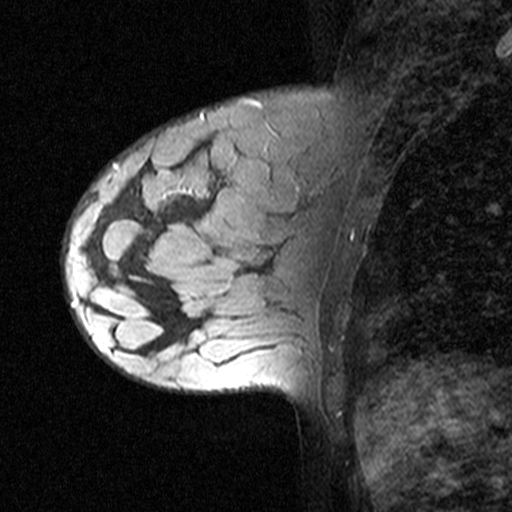
Breast MRI (dynamic contrast-enhanced), one sagittal slice; position 14 of 44 along the scan axis; dynamic contrast-enhanced study with each time point stored as its own series, time point 2 of 3 at this slice position (early post-contrast, ordered by acquisition time); 1.5 T; TE 4.5 ms, TR 11 ms; 3 mm slice thickness; 512 × 512 image matrix, field of view 200 × 200 mm. Patient: female, 27 years. From the clinical record (not read from this slice): setting: breast cancer imaged before/during neoadjuvant chemotherapy; receptor status: HR-positive, HER2-negative.
Structures marked on this image (semi-automatically segmented with operator editing):
- analysis volume of interest (the breast-tissue region the enhancement analysis was run in; not a lesion): bounding box [x1, y1, x2, y2] px = [62, 162, 163, 271]
- tumour enhancement mask (voxels above the 90 % enhancement threshold inside the analysis volume of interest): [103, 165, 121, 243]